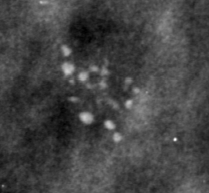
Cropped region of a digitized screen-film mammogram centred on a radiologist-marked abnormality; left breast; MLO view.
Finding: calcifications, morphology pleomorphic, distribution clustered; BI-RADS assessment category 4; subtlety rating 4 on a 1 (subtle) to 5 (obvious) scale; pathology result (as recorded, not read from the image): malignant.